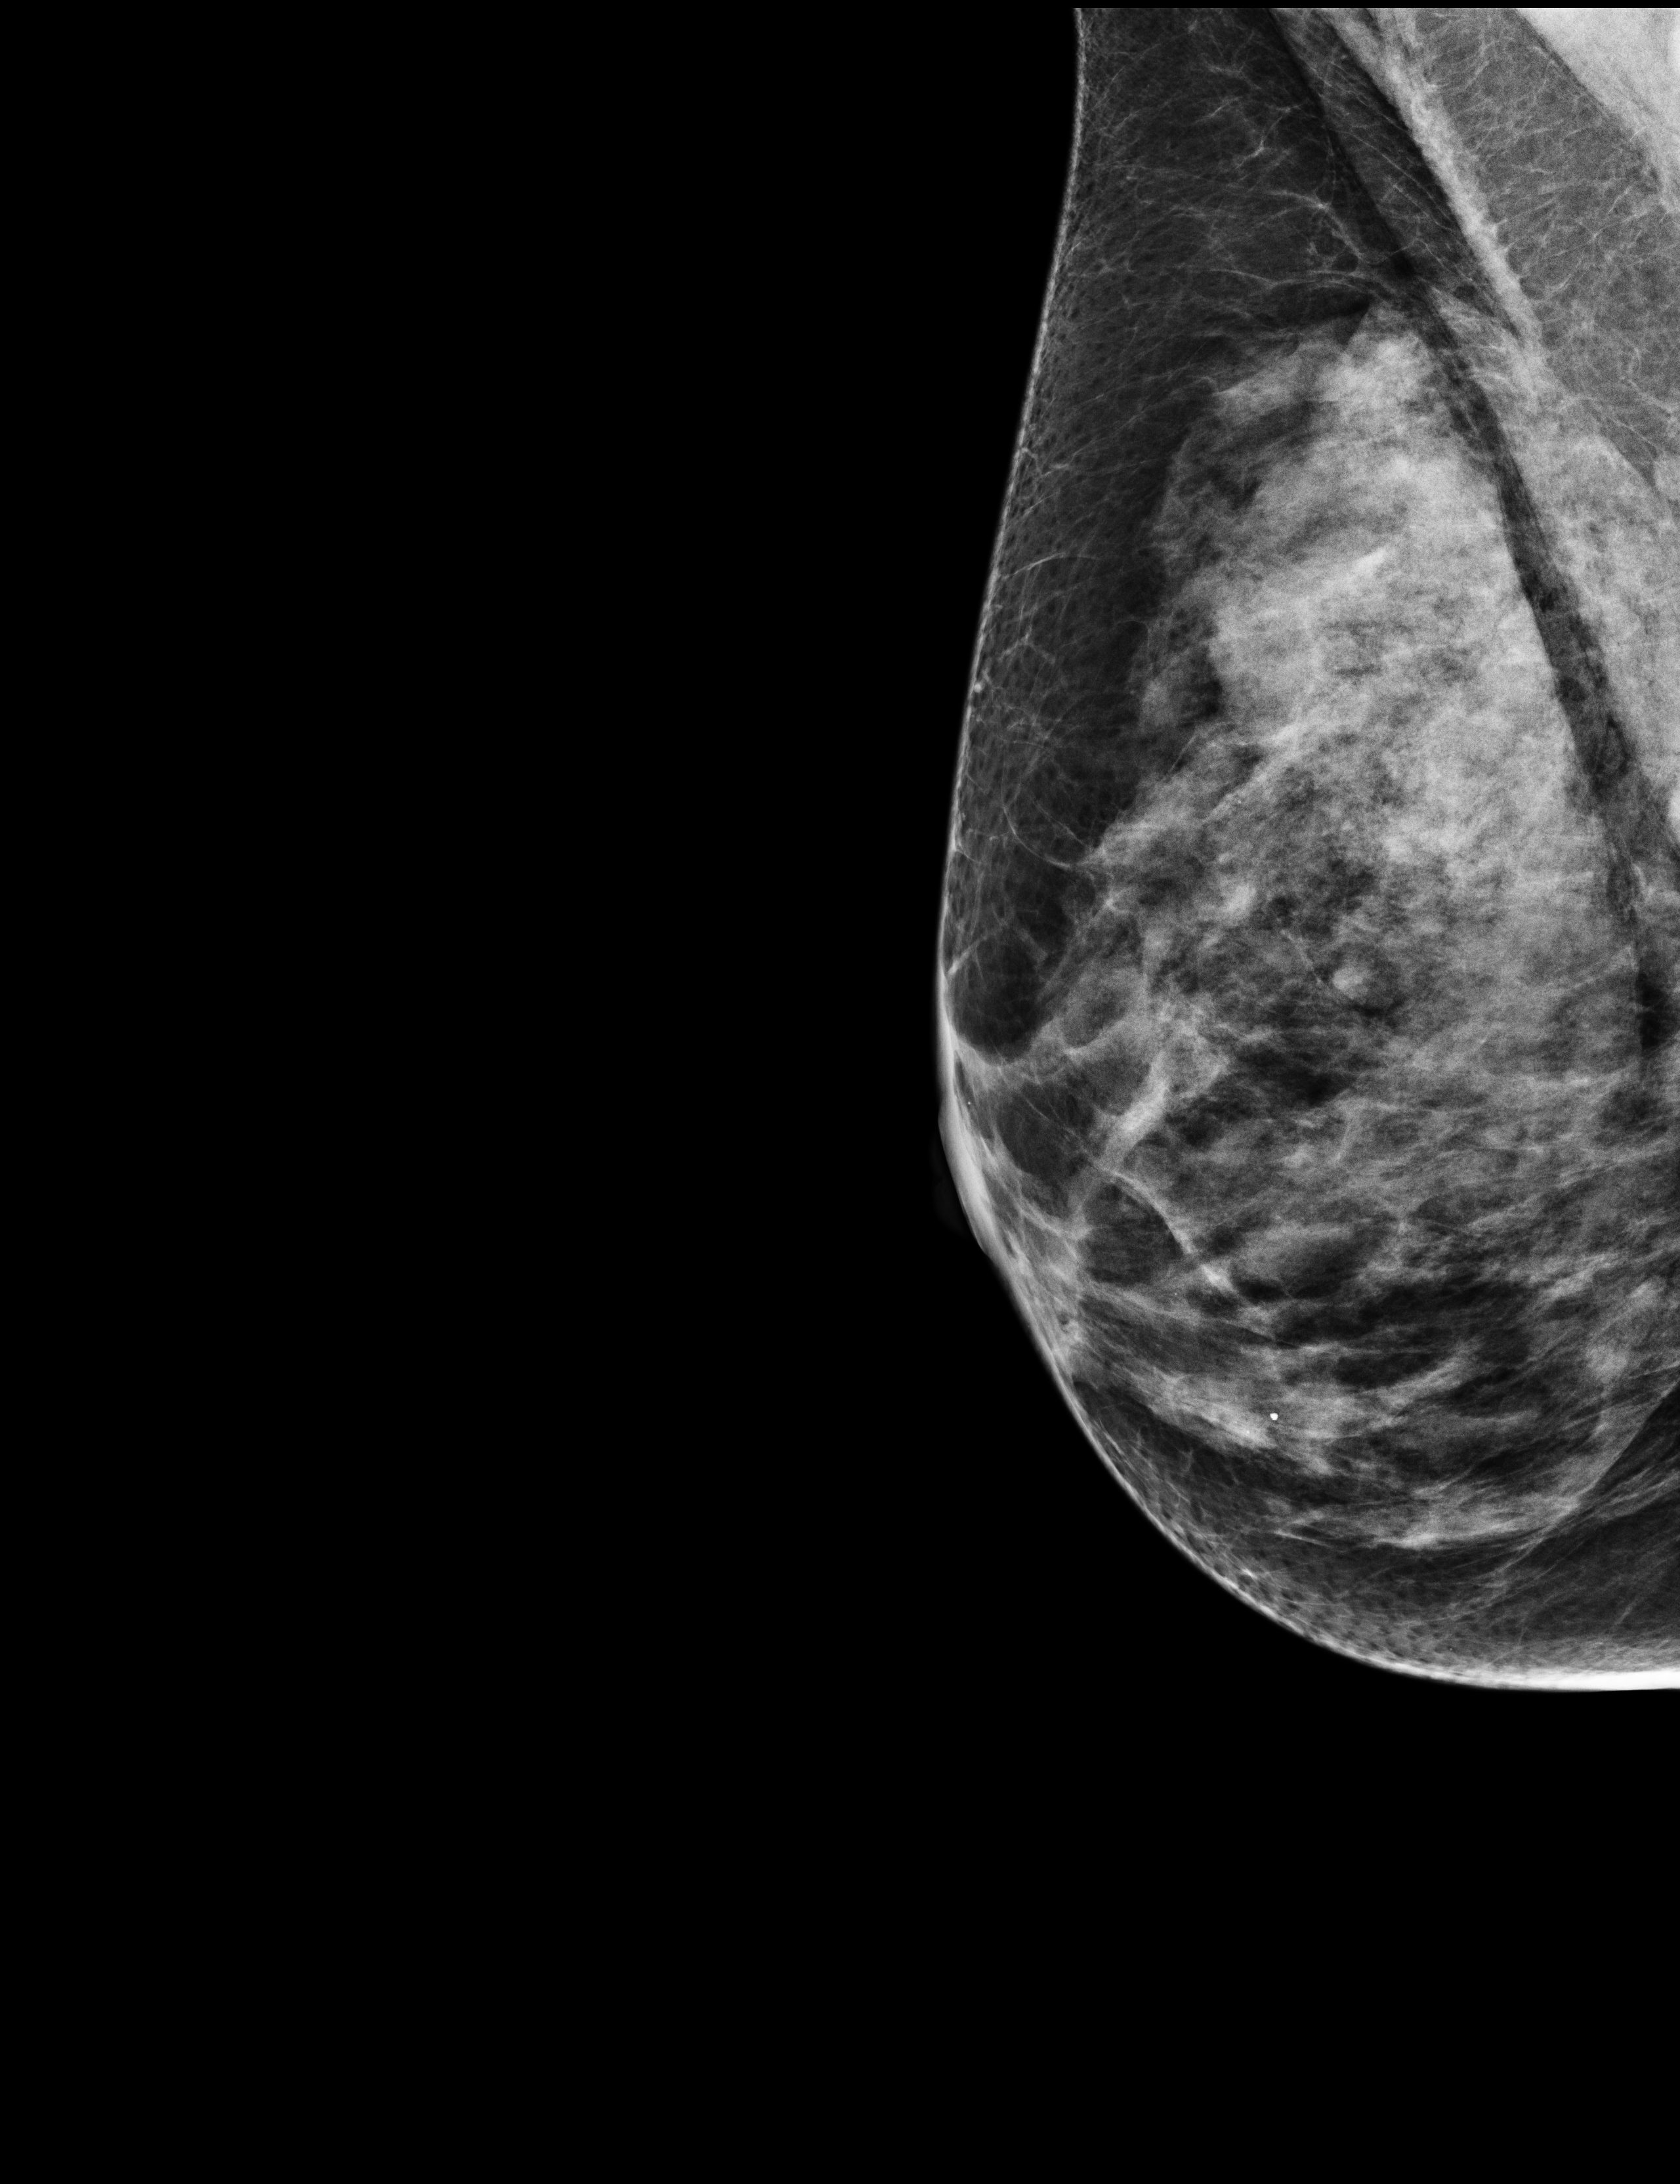
Screening examination; system: Selenia Dimensions.
Image type: full-field digital mammogram. Breast: right. Projection: medio-lateral oblique projection.